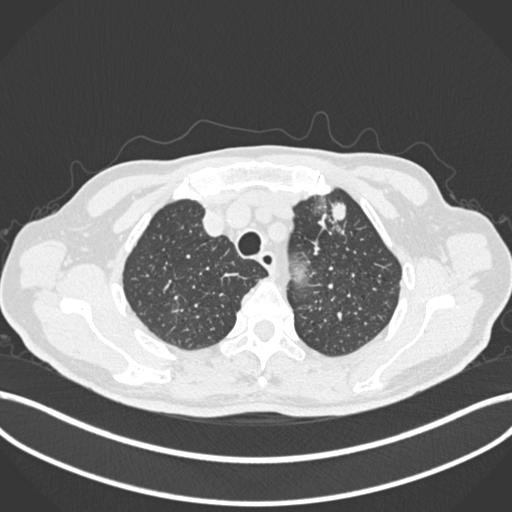
Chest CT, one axial slice; position 211 of 261 along the scan axis; lung window (W 1500 / L -600 HU); 512 × 512 image matrix. Male patient, age 74 years. From the clinical record (not read from this slice): clinical TNM (as recorded): T2b N0 M1c.
Outlined on this slice (rectangle marked by the reading radiologist):
- lung tumour (recorded histology: adenocarcinoma): bounding box (x1, y1, x2, y2) in pixels: (314, 190, 355, 241)